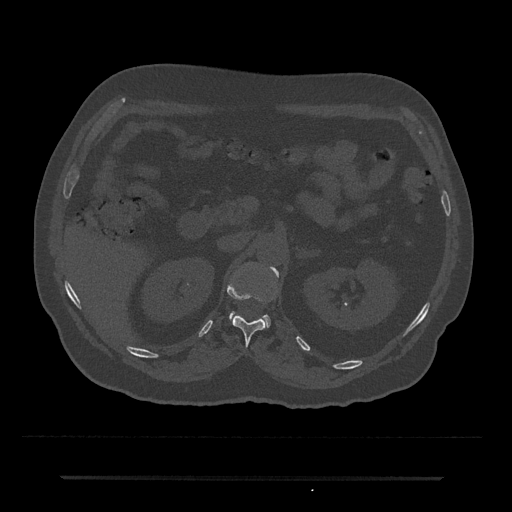
CT including the spine, one axial slice; reconstruction kernel Br40s/3; bone window (W 1800 / L 400 HU); 0.5 mm slice thickness; 512 × 512 image matrix, field of view 437 × 437 mm. Patient: male, 69 years. Case-level facts recorded for this patient, not image findings: primary cancer: prostate.
Outlined on this slice (semi-automatically segmented with operator editing):
- L1 vertebra: bounding box <230,267,279,326> (left, top, right, bottom; pixels)
- T12 vertebra: <227,271,277,345>